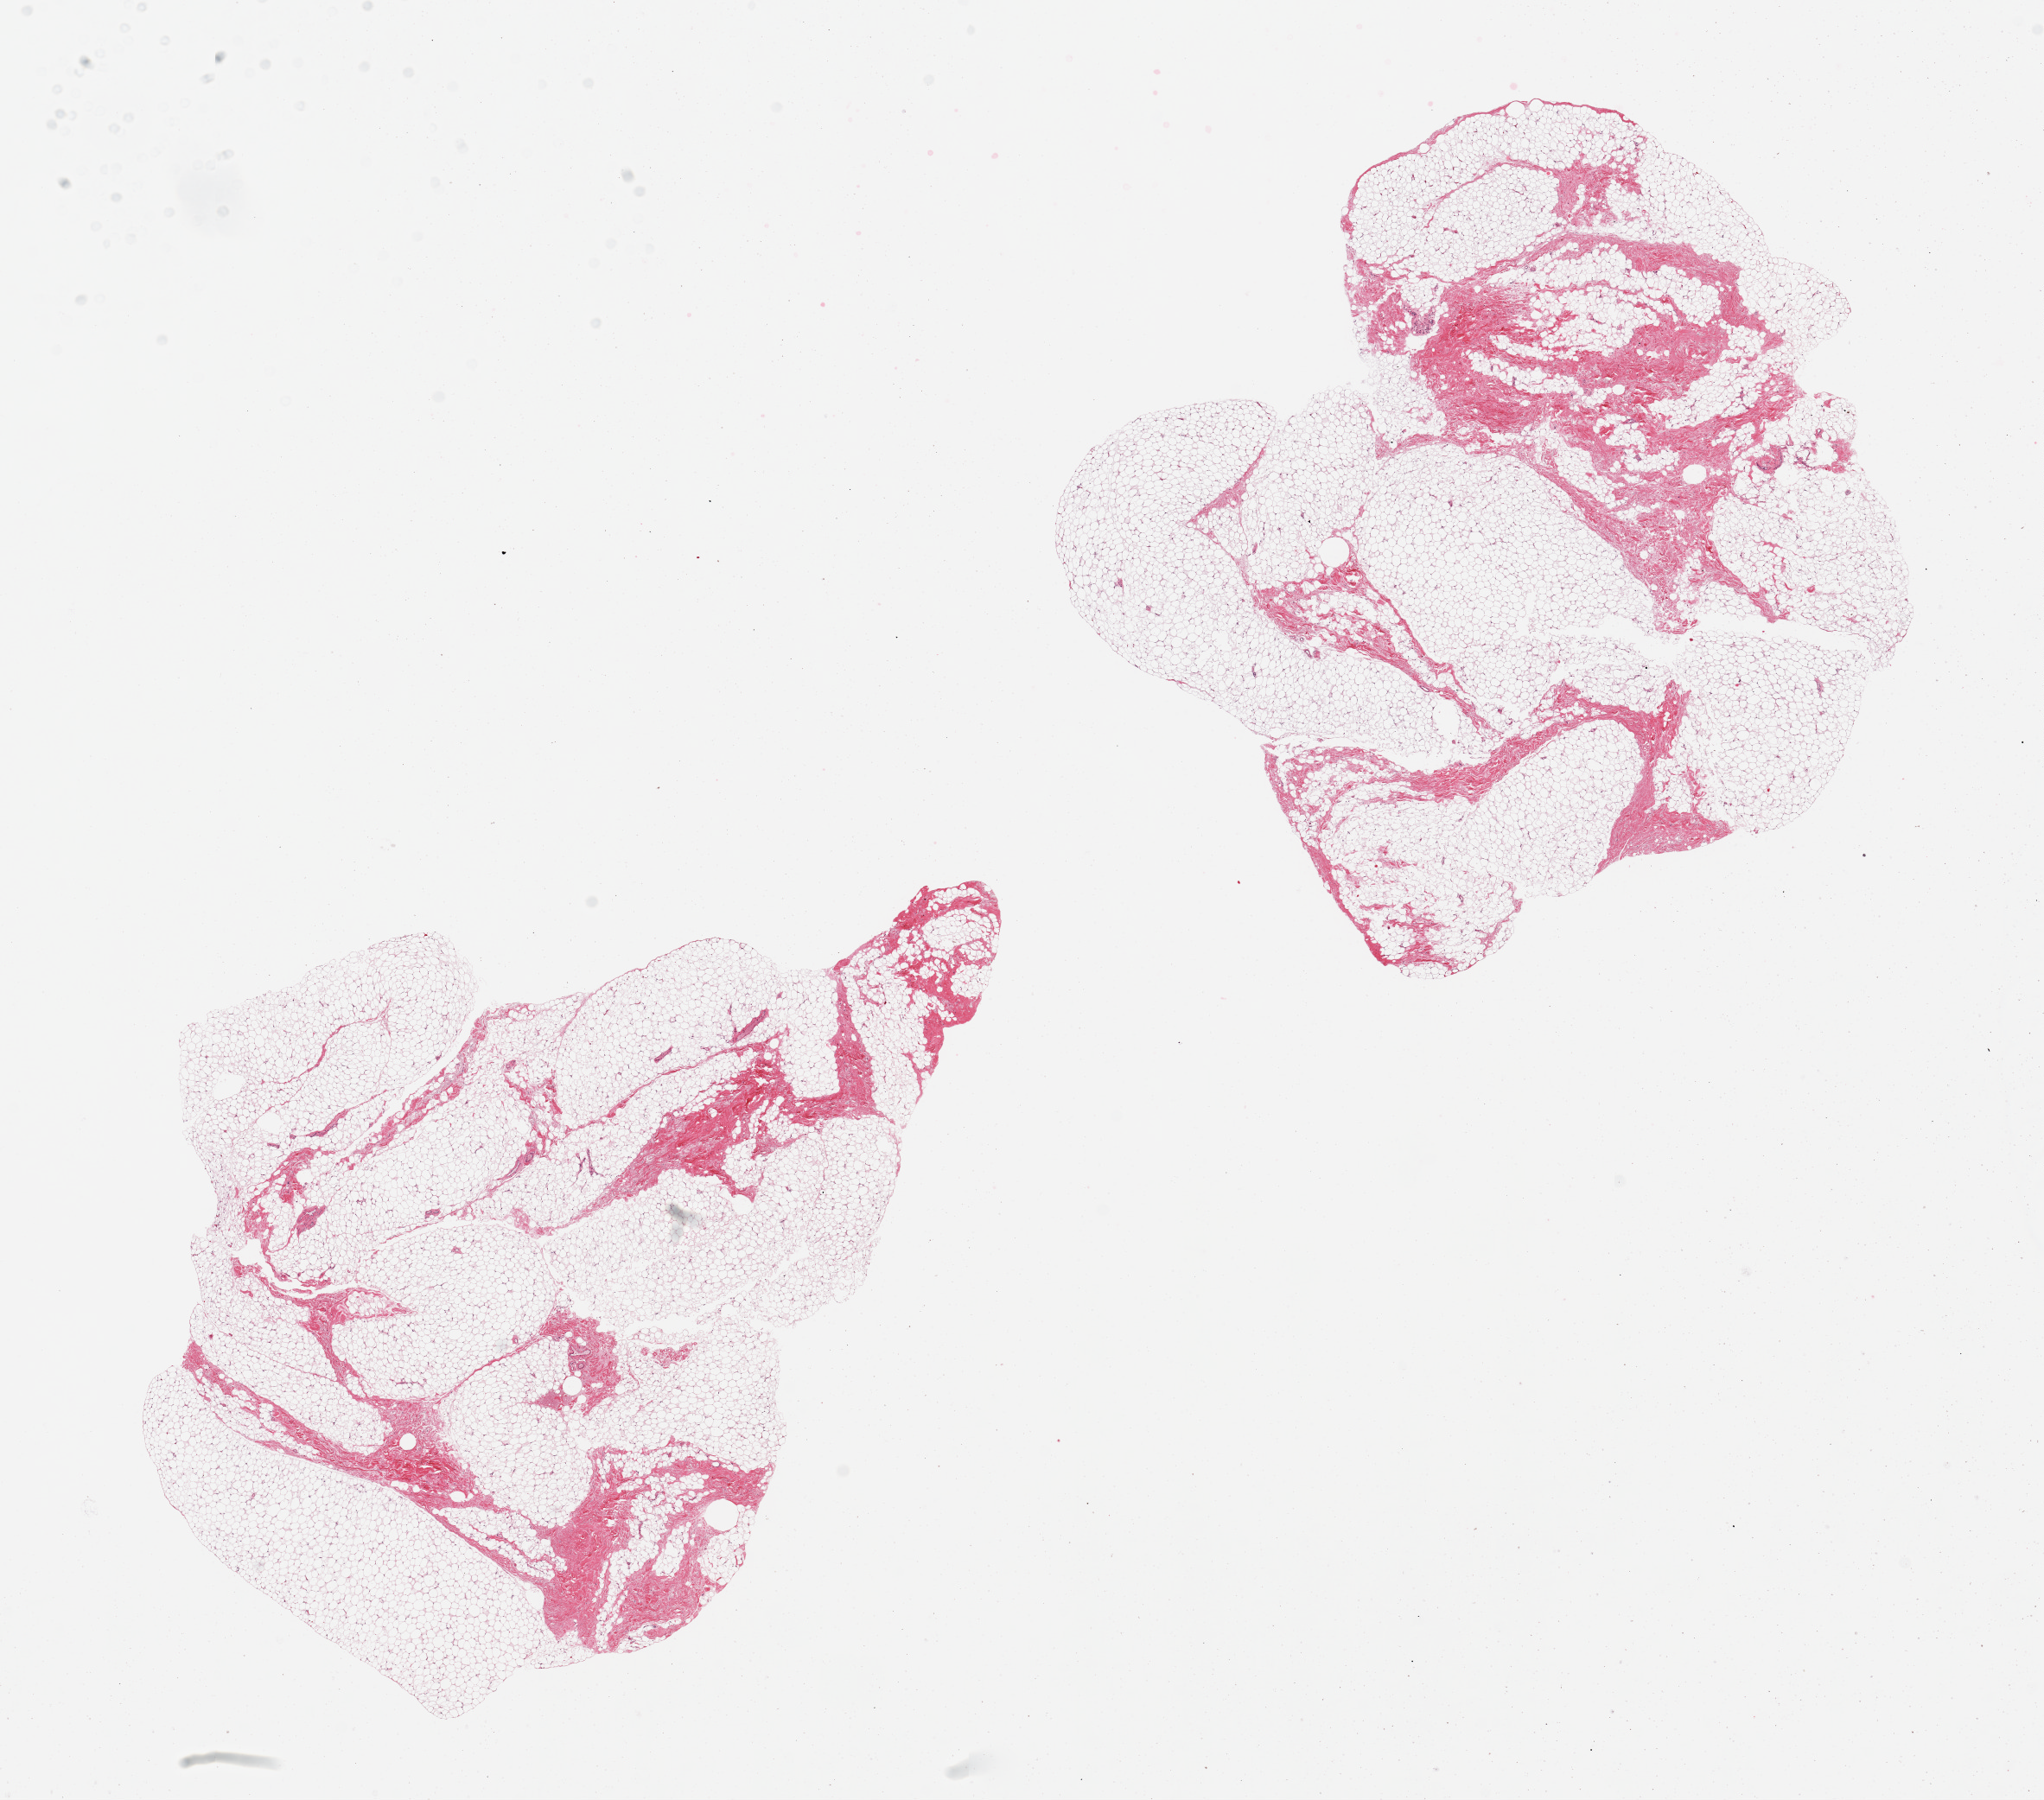
Digitized hematoxylin and eosin (H&E)-stained section, low-resolution overview of the scanned area, about 18.7 x 16.5 mm; PAXgene-fixed, paraffin-embedded tissue; section of breast (target tissue); donor tissue sample. Donor sex: male.
Review note (as recorded): 2 pieces, fibroadipose stroma only, no ductal elements noted.